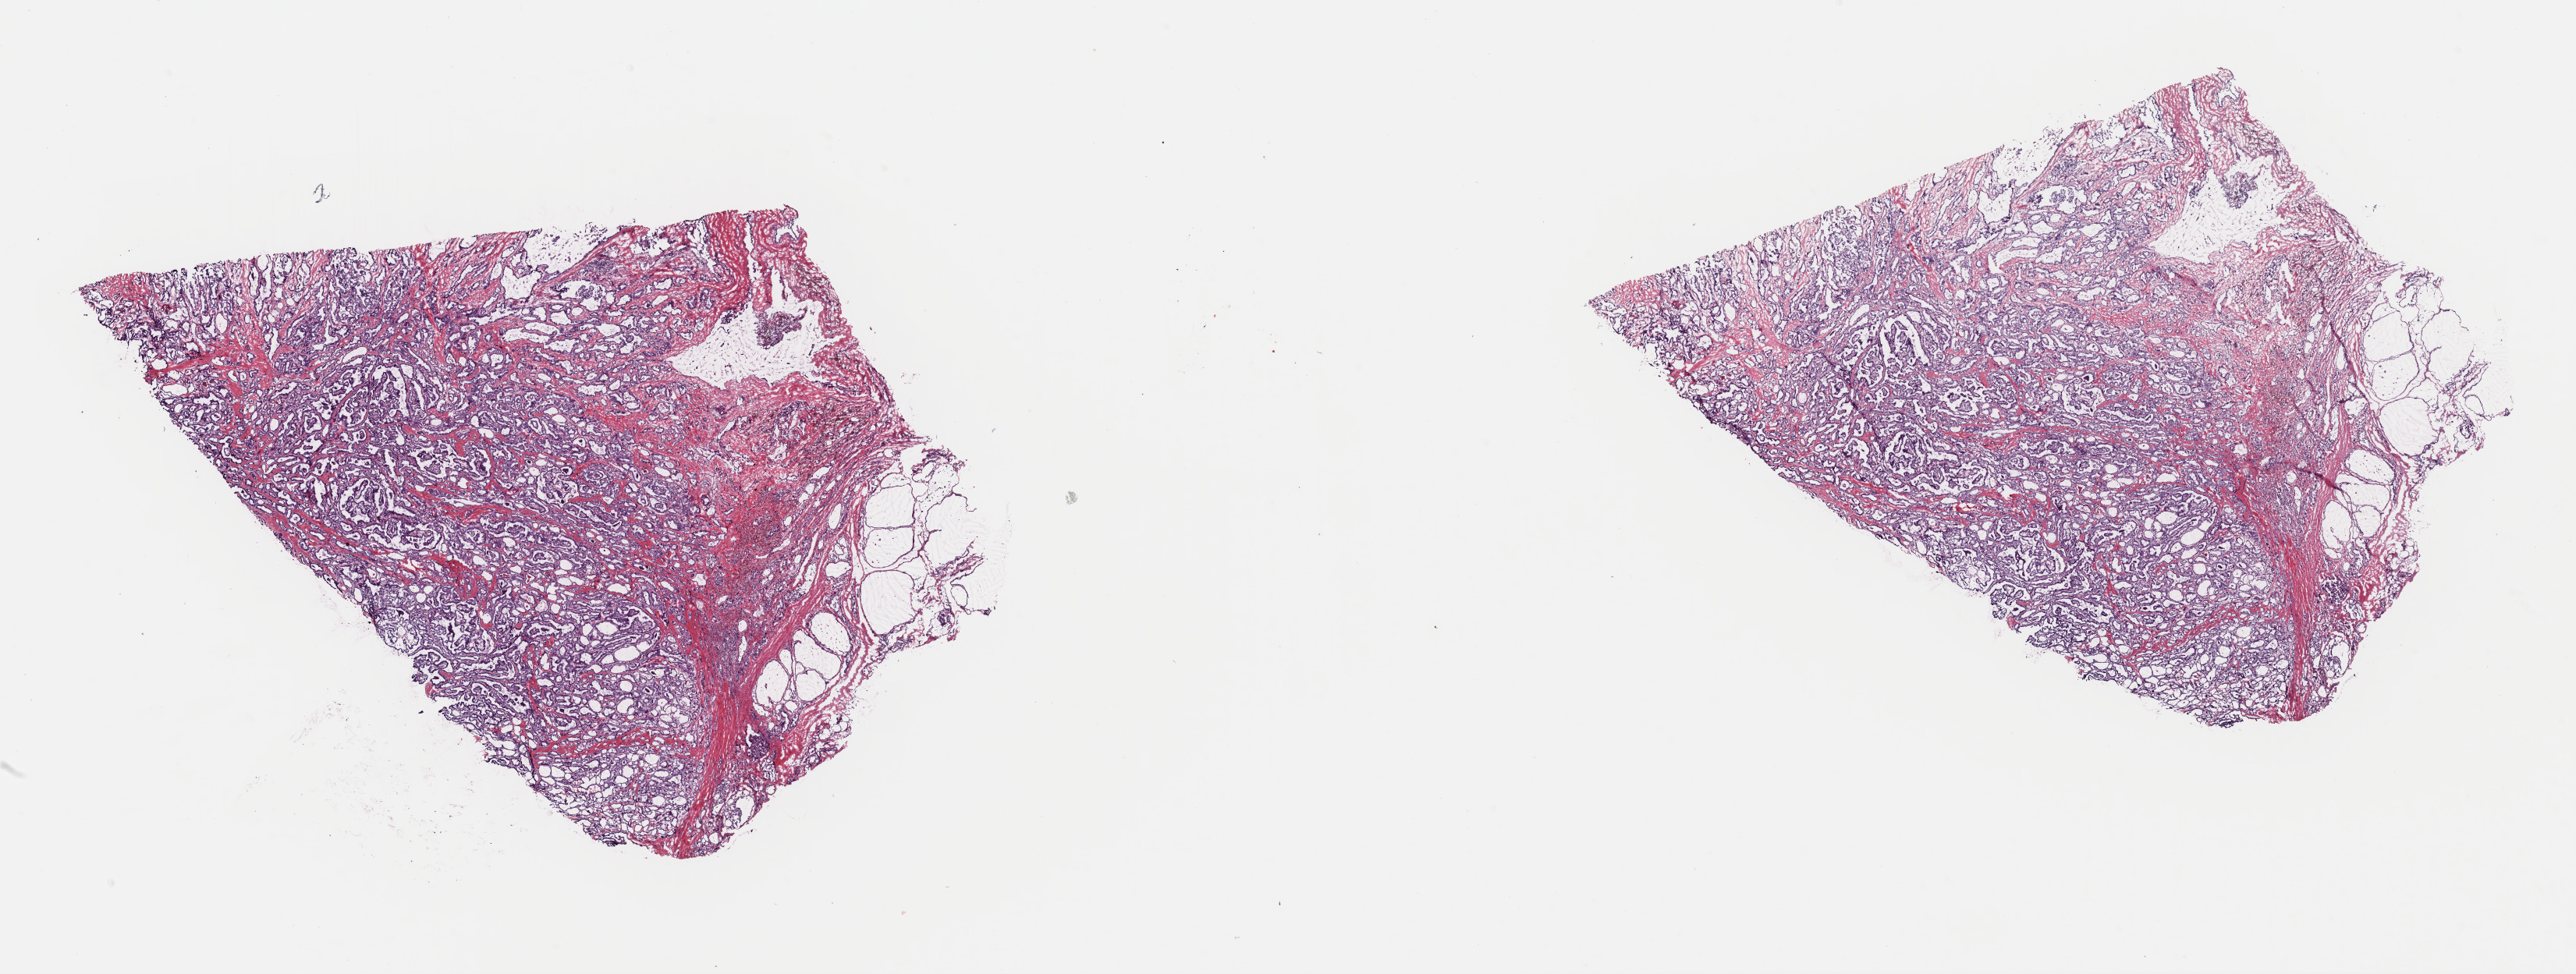
Digitized H&E-stained tissue section (whole slide) — whole scanned area (about 26.1 x 9.9 mm, slide scanned at 40x) shown as a low-resolution overview. Frozen section. Thyroid, primary tumour sample. Patient: male, age at initial diagnosis 45 years. Slide review estimates, as recorded: tumour cells 90%, tumour nuclei 80%, normal cells 0%, stromal cells 10%, necrosis 0%. Inflammatory infiltration, as recorded: lymphocyte infiltration 2%, monocyte infiltration 1%, neutrophil infiltration 0%.
Laterality: bilateral. Histologic diagnosis: Papillary adenocarcinoma, NOS. AJCC pathologic stage: III (7th edition).